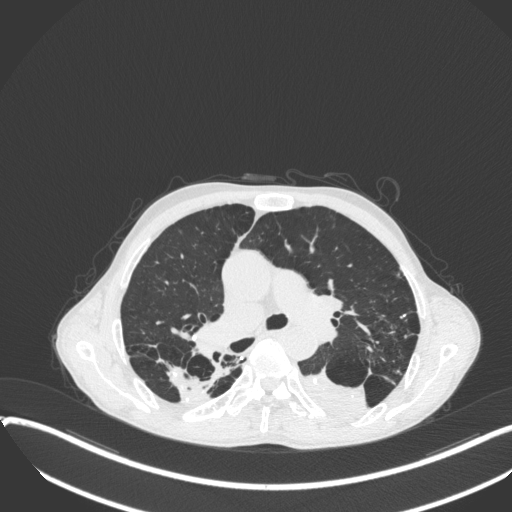
Chest CT, one axial slice. Position 240 of 400 along the scan axis. Reconstruction kernel B31f. Lung window (W 1500 / L -600 HU). 512 × 512 image matrix, field of view 400 × 400 mm. Male patient, age 57 years. From the clinical record (not read from this slice): clinical TNM (as recorded): T4 N0 M0.
Annotated regions visible in this slice (bounding box drawn by a radiologist):
- lung tumour (recorded histology: squamous cell carcinoma): box from (x=300, y=364) to (x=376, y=421) px